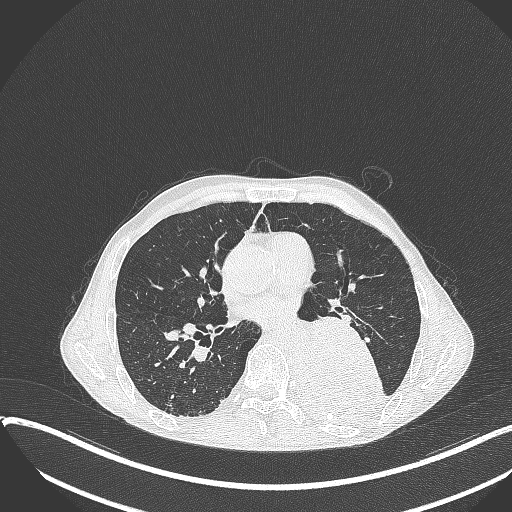
Chest CT, one axial slice; slice 188 of 401 in the series (ordered by position); reconstruction kernel B70f; 120 kVp; lung window (W 1500 / L -600 HU); 512 × 512 image matrix. Patient: male, 57 years. From the clinical record (not read from this slice): clinical TNM (as recorded): T4 N0 M0.
Outlined on this slice (rectangle marked by the reading radiologist):
- lung tumour (recorded histology: squamous cell carcinoma): box from (x=287, y=313) to (x=390, y=425) px